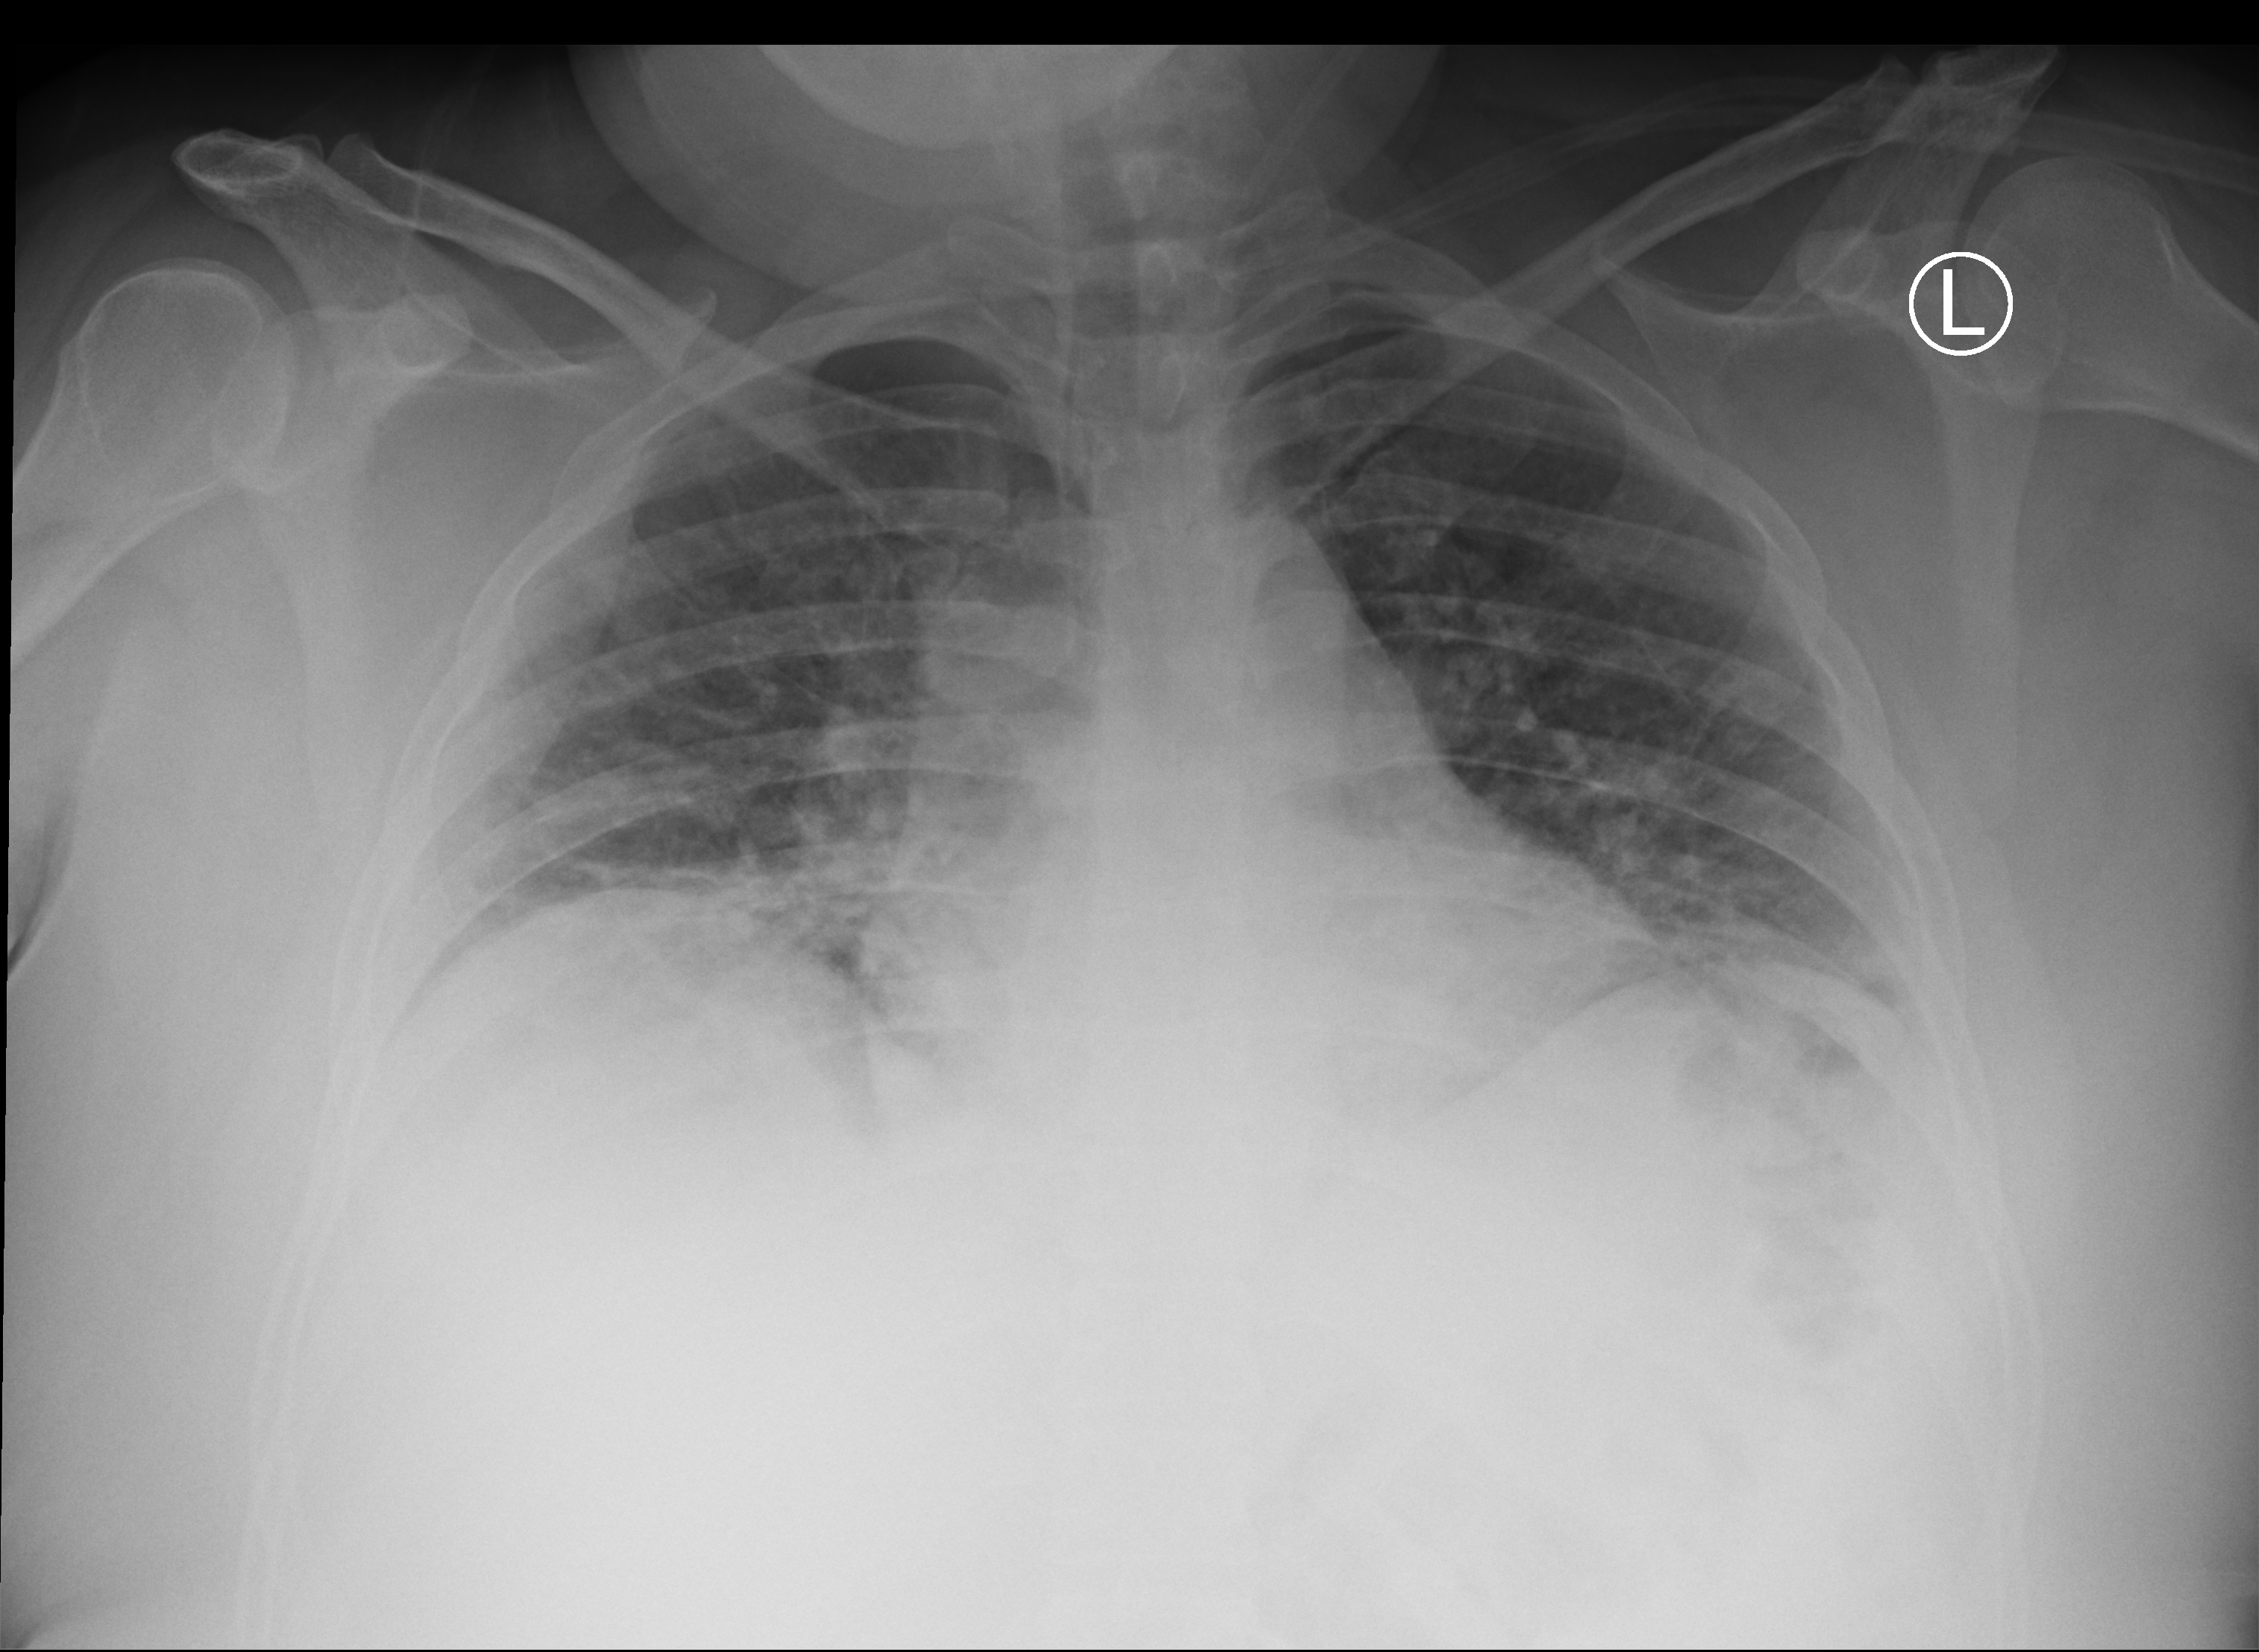
Portable chest radiograph. Patient hospitalised with COVID-19; female, aged 18–59 years.
Admission-level facts for this patient (not findings on this image; timing relative to this image not recorded): hypertension (admission record): no; admitted to intensive care during this hospital stay: no.